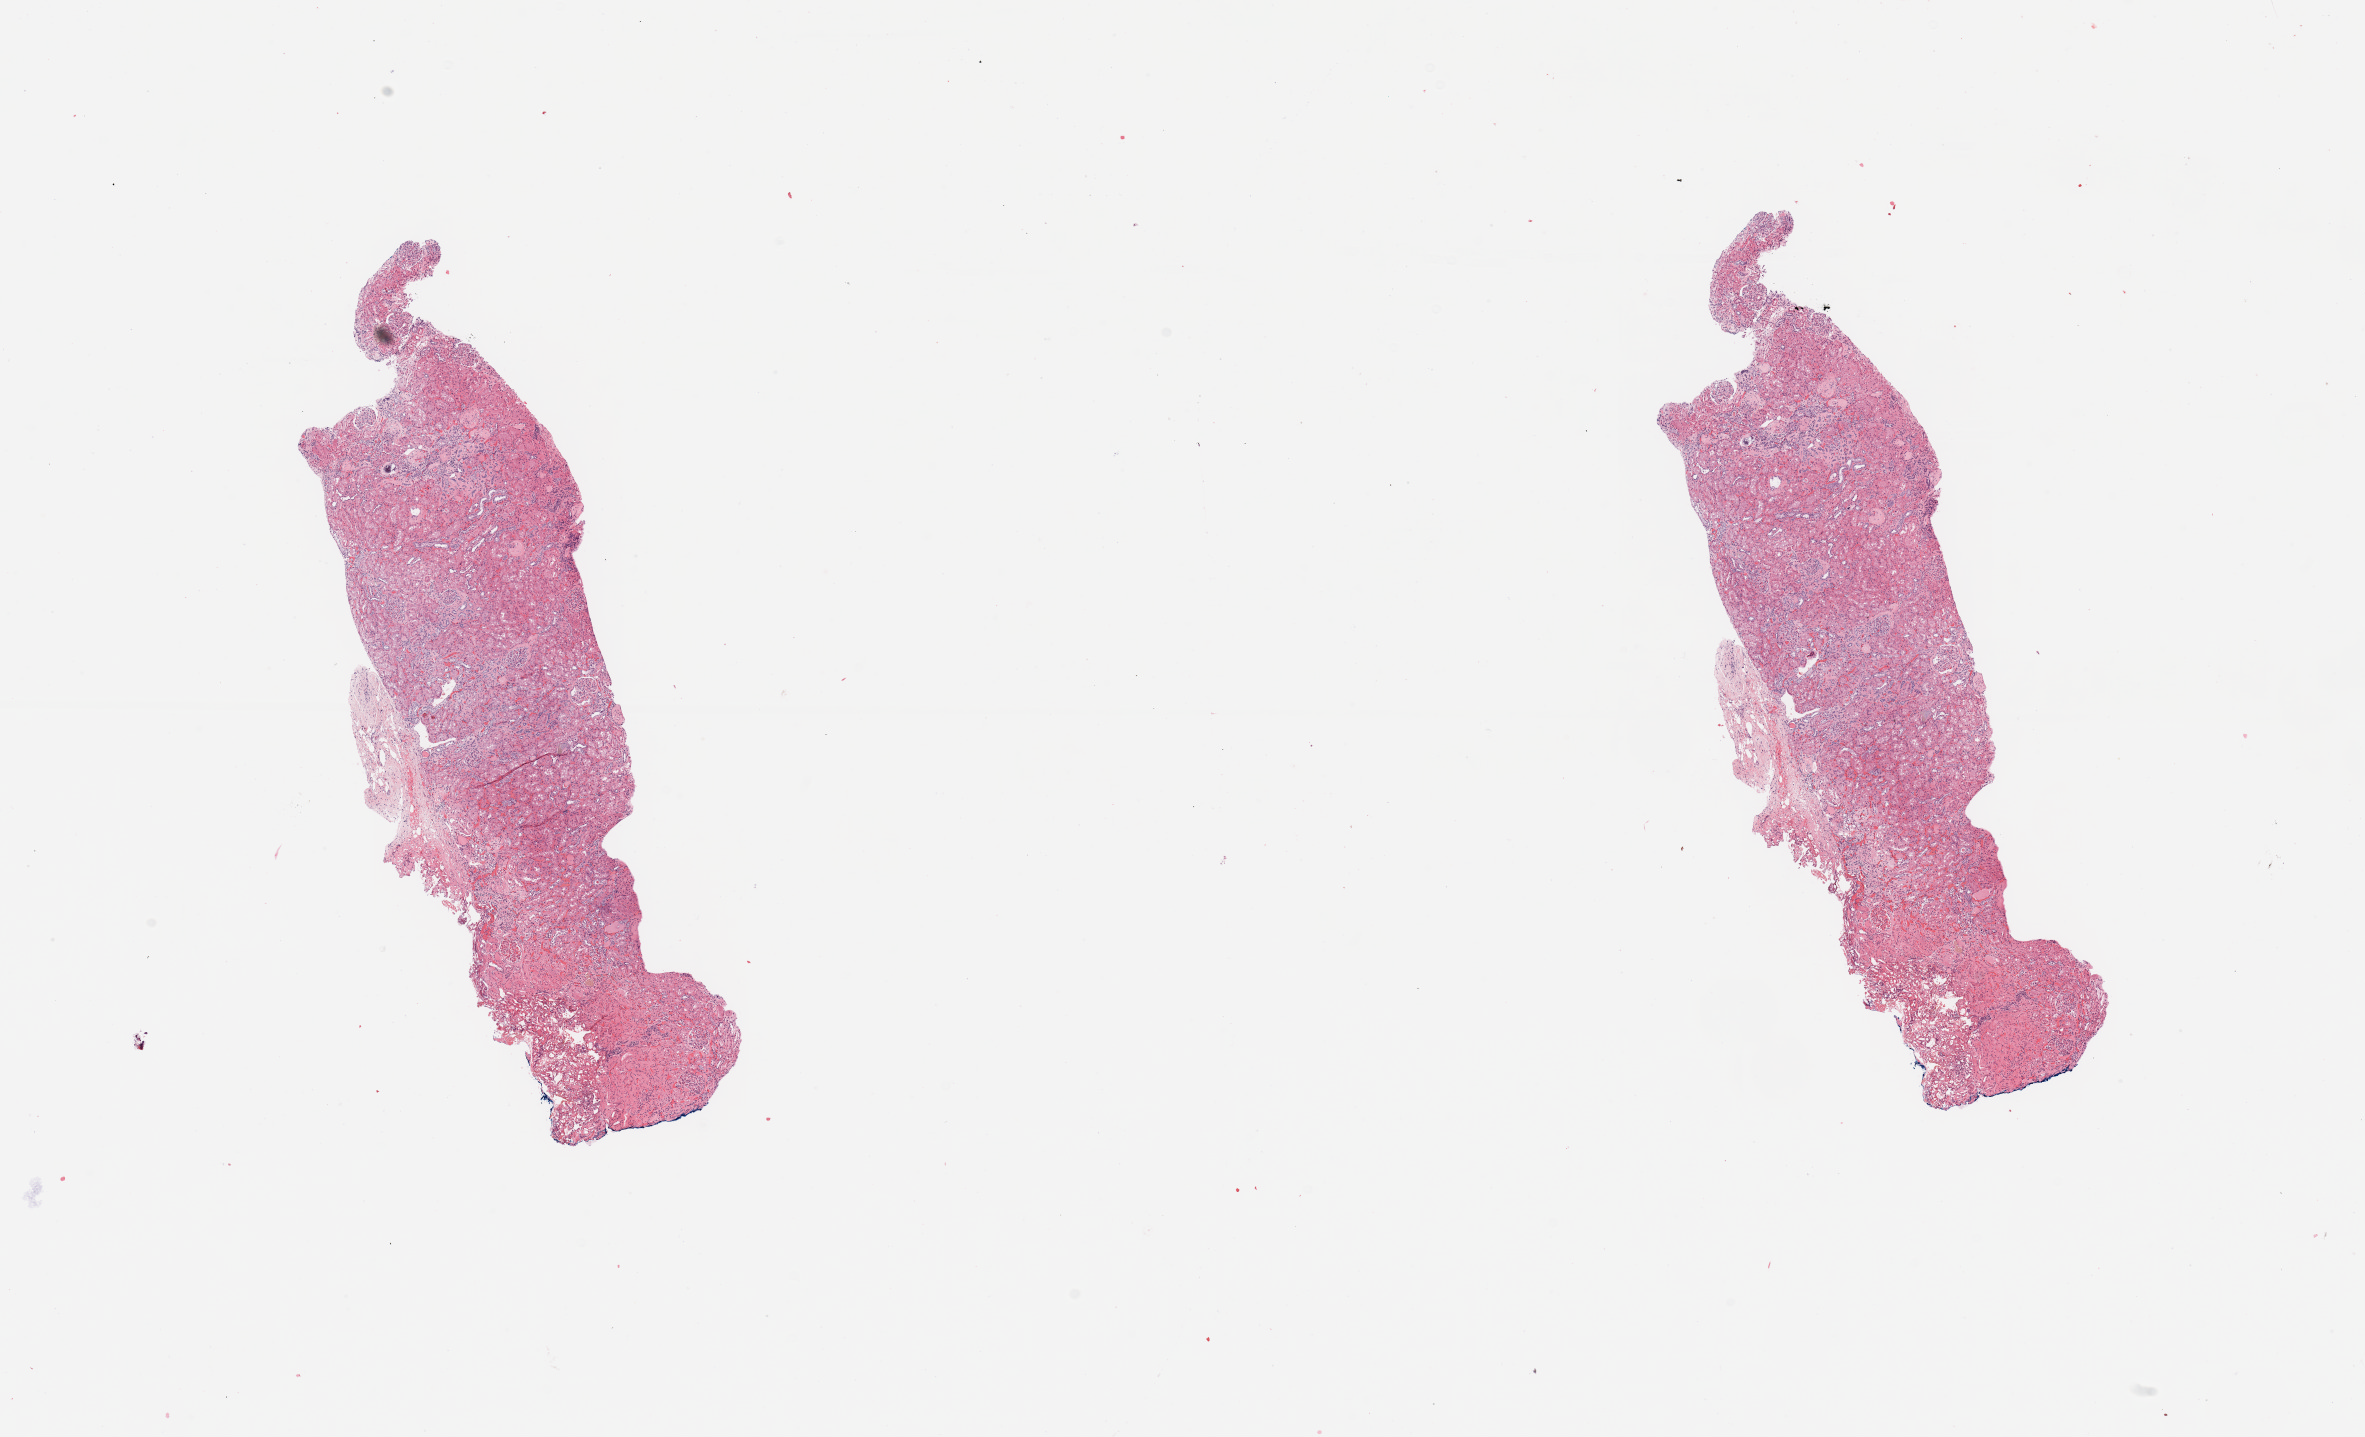
Hematoxylin and eosin (H&E) stained whole-slide image, shown as a low-resolution overview of the whole scanned area (about 18.7 x 11.4 mm). Normal (non-tumour) tissue sample, sampled site: kidney. Patient: female, age 70 years.
This section: normal (non-tumour) tissue from the same patient. Patient diagnosis: Renal cell carcinoma, NOS.